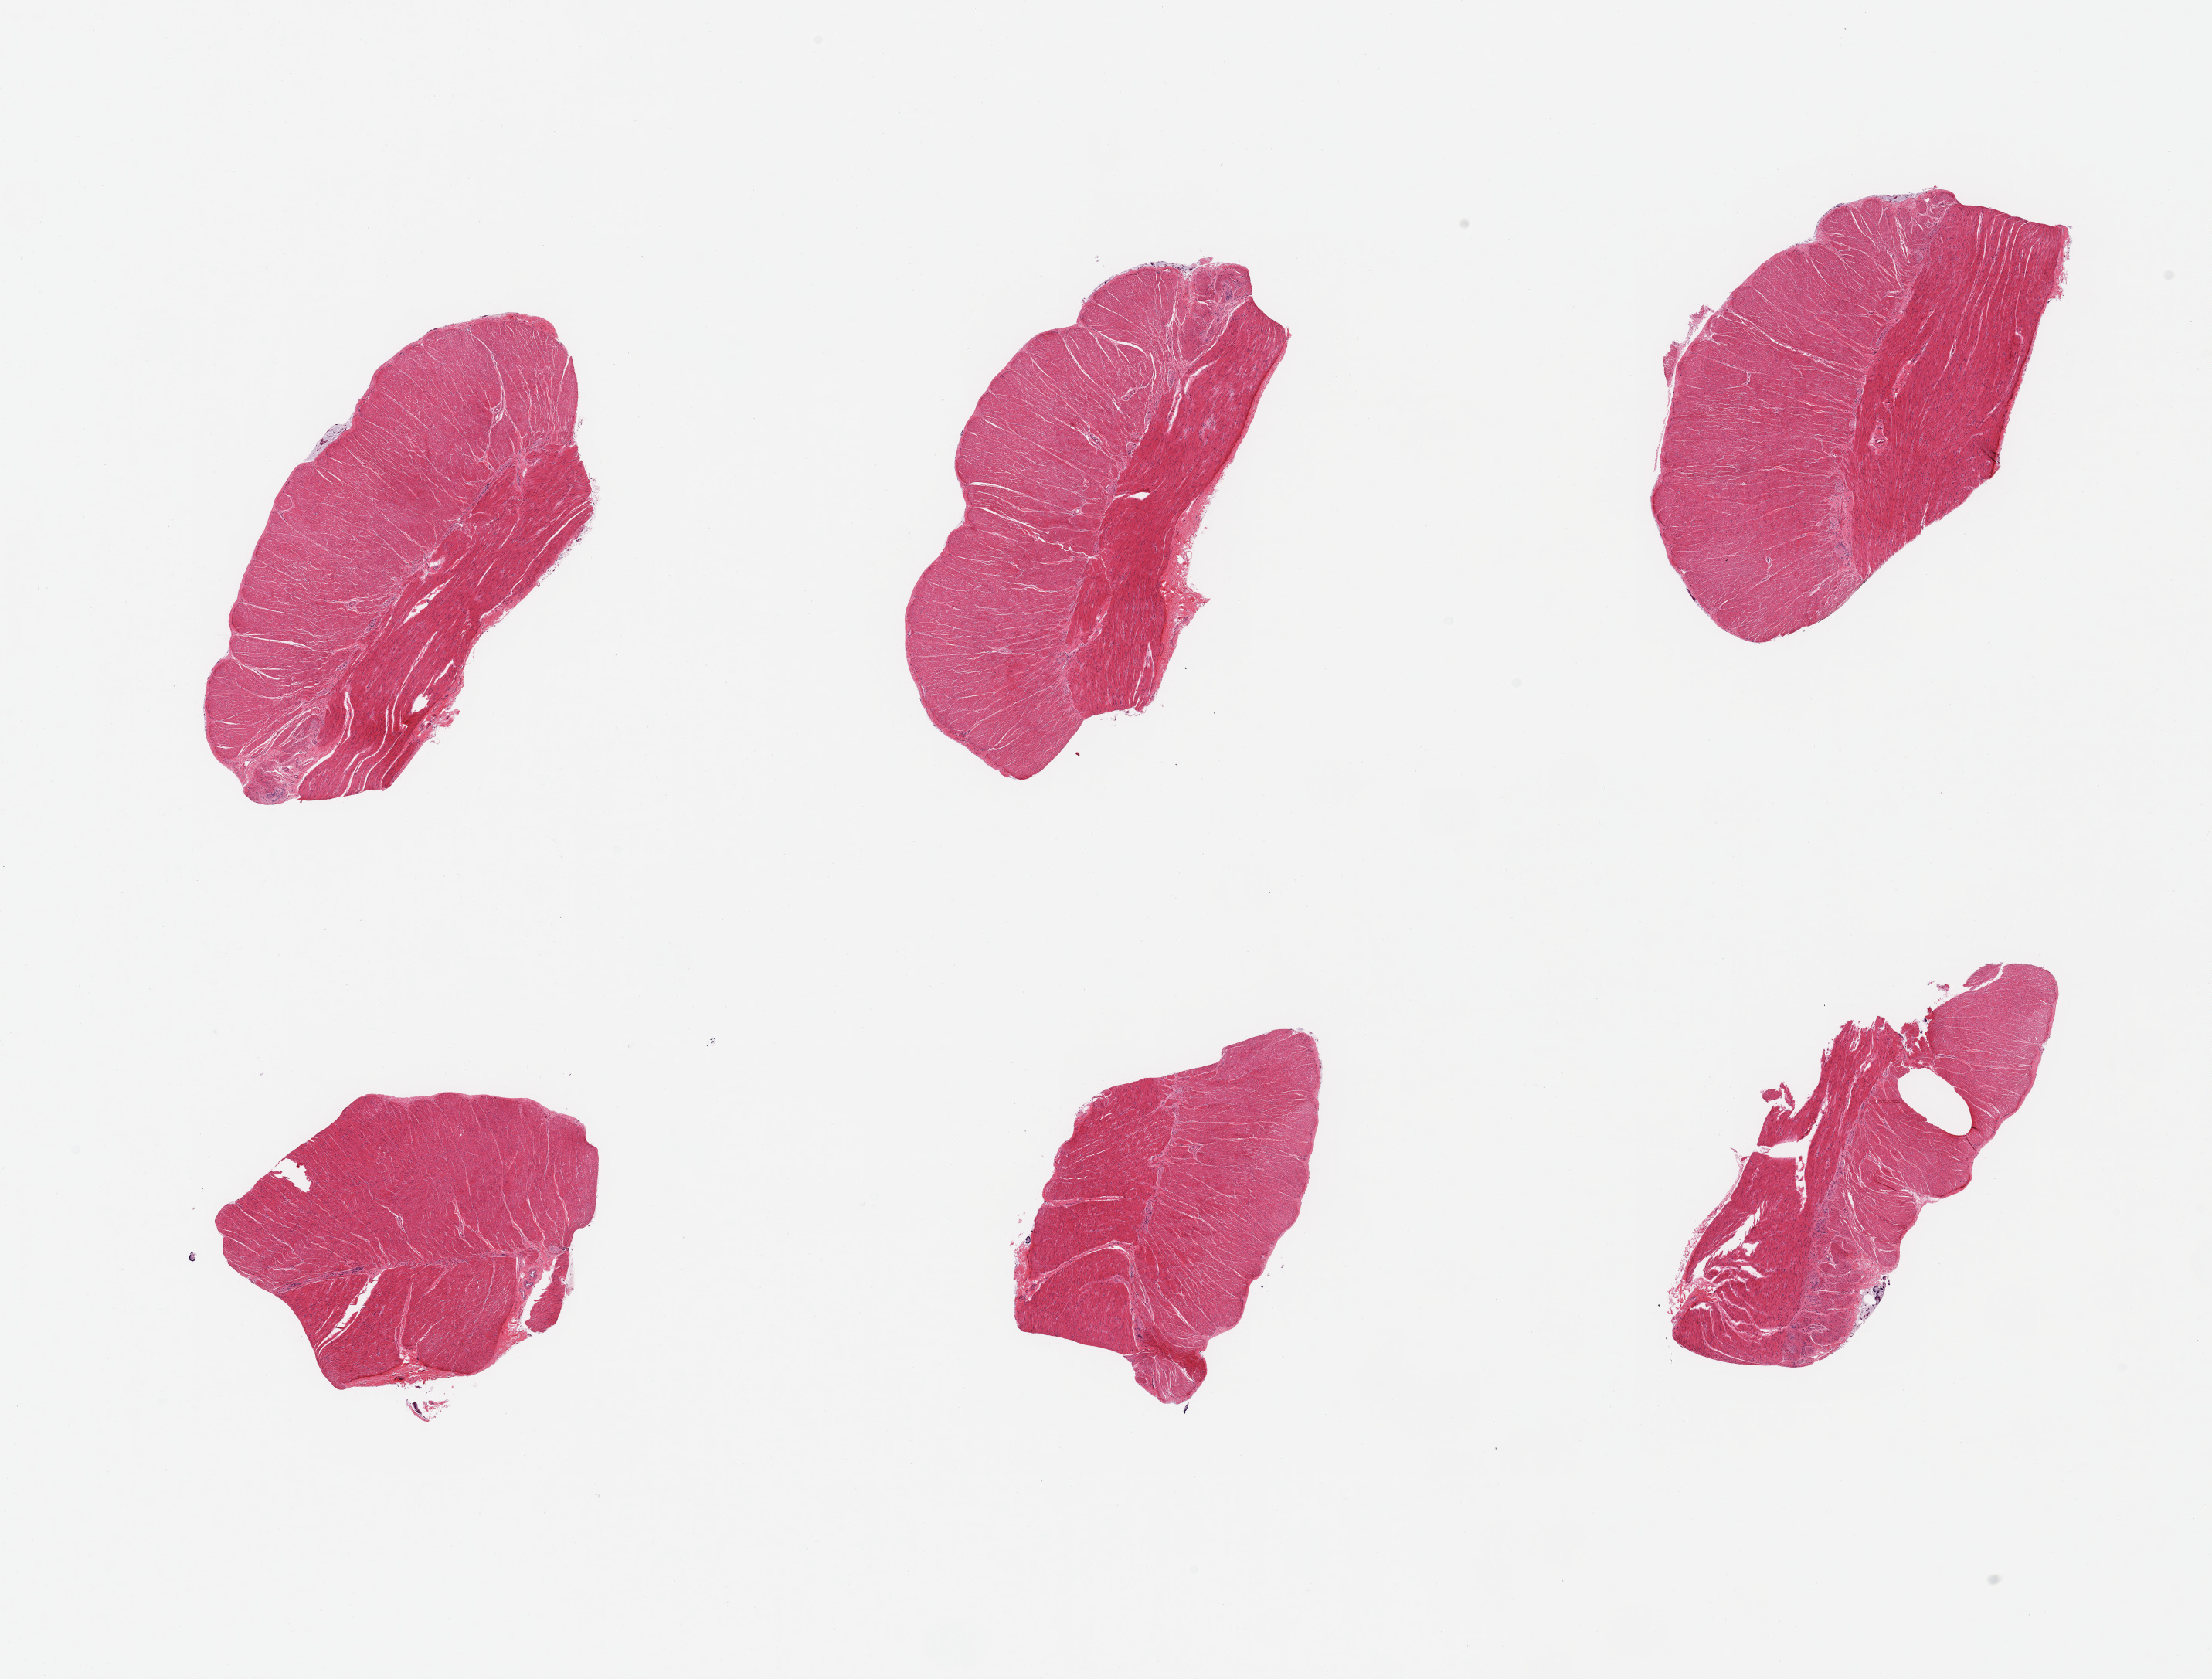
Digitized haematoxylin and eosin-stained section — whole scanned area (about 22.6 x 17.2 mm) shown as a low-resolution overview; PAXgene-fixed, paraffin-embedded tissue; target tissue: sigmoid colon; donor tissue sample. Donor: female.
Review note (as recorded): 6 pieces; well dissected muscle.